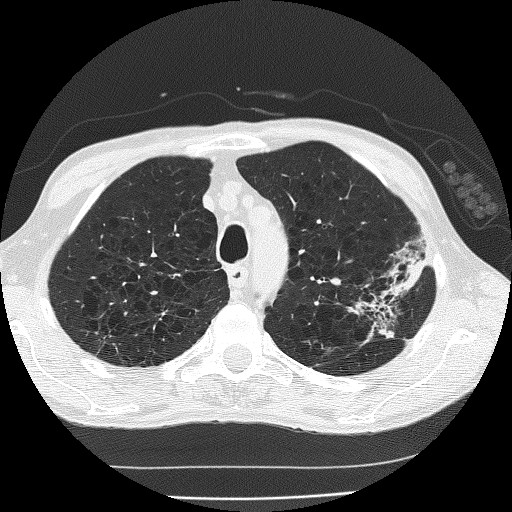
Low-dose screening chest CT, one axial slice. Slice 145 of 185 in the series (ordered by position). Reconstruction kernel FC51. 120 kVp. Lung window (W 1500 / L -600 HU). 2 mm slice thickness. 512 × 512 image matrix, field of view 320 × 320 mm.
Annotated regions visible in this slice (expert manual segmentation):
- lesion 1 (tumor, upper lobe of left lung): bounding box <384,257,425,298> (left, top, right, bottom; pixels)